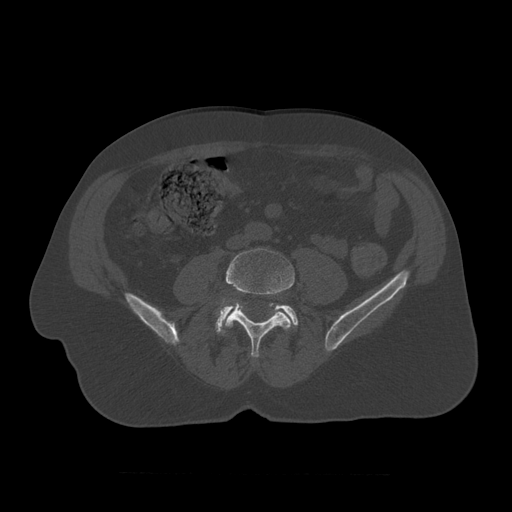
CT including the spine, one axial slice. Position 271 of 450 along the scan axis. Reconstruction kernel STANDARD. 120 kVp. Bone window (W 1800 / L 400 HU). 1.25 mm slice thickness. 512 × 512 image matrix, field of view 405 × 405 mm. Patient age 75 years. Case-level facts recorded for this patient, not image findings: primary cancer: prostate.
Structures marked on this image (semi-automatically segmented with operator editing):
- L4 vertebra: bounding box [x1, y1, x2, y2] px = [216, 248, 295, 358]
- L5 vertebra: [215, 302, 299, 335]